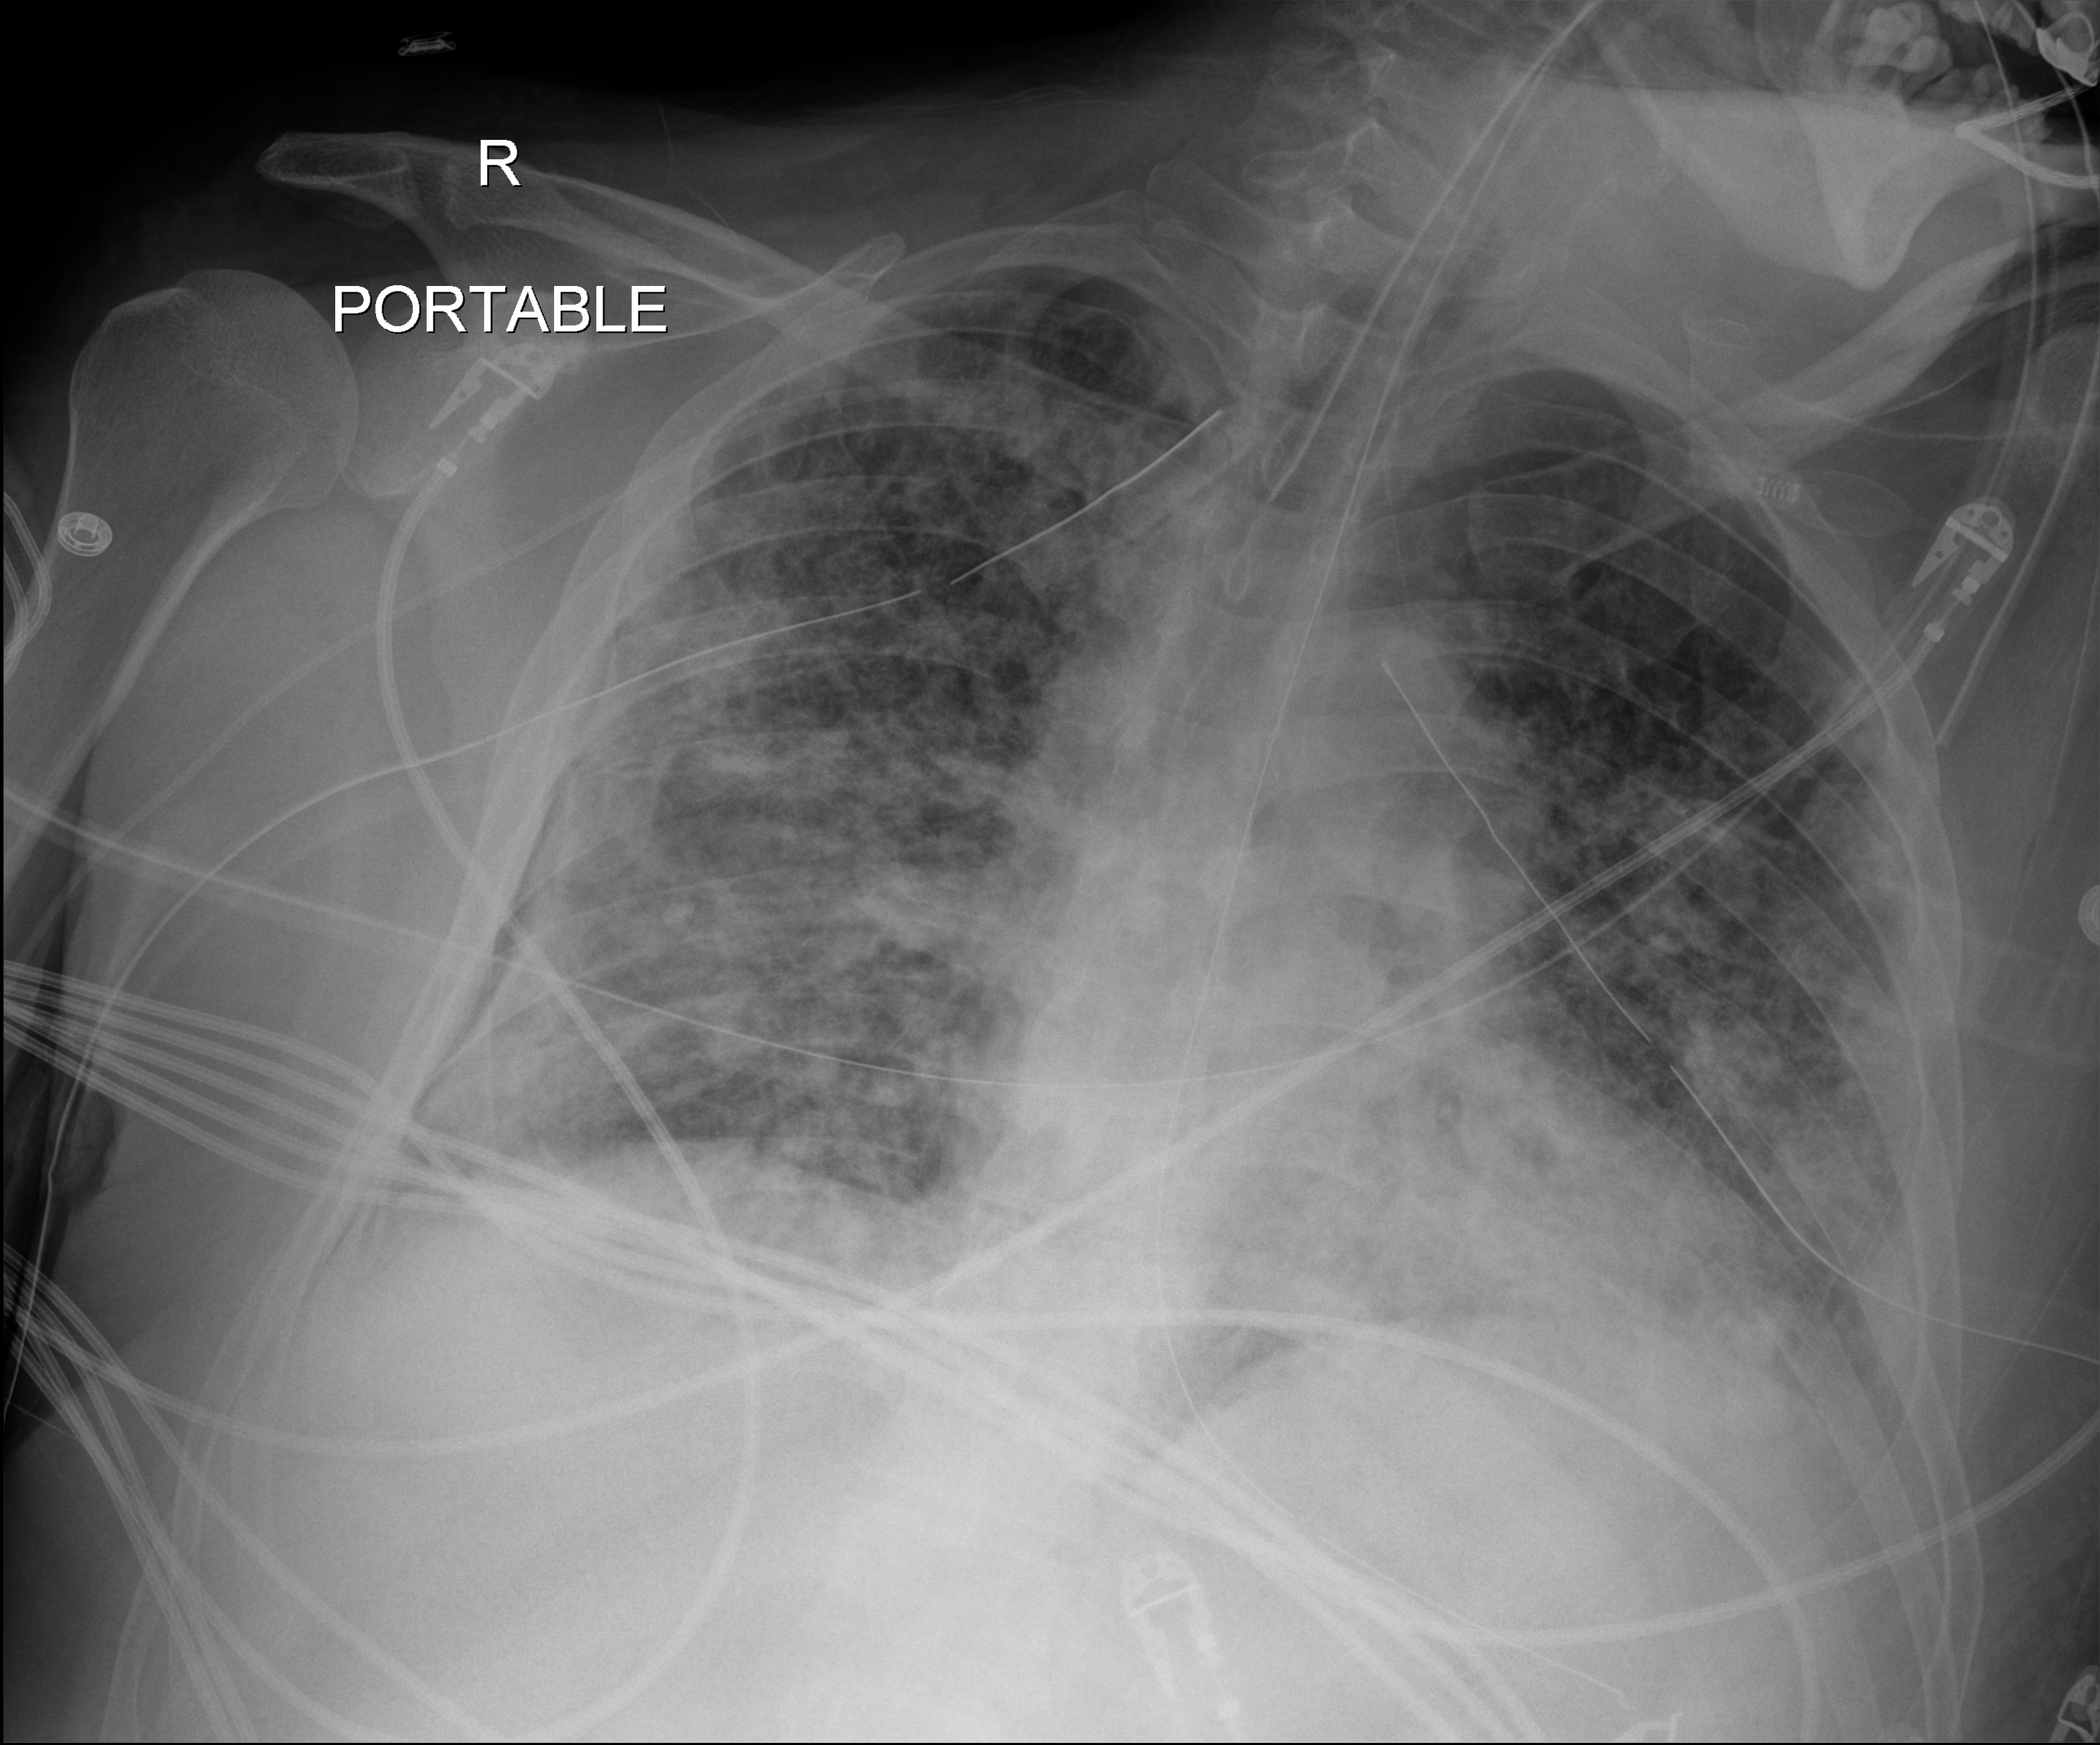
Portable chest radiograph; anteroposterior (AP) projection. Male patient hospitalised with COVID-19, age 18–59 years.
Admission-level facts for this patient (not findings on this image; timing relative to this image not recorded): admitted to intensive care during this hospital stay: yes.